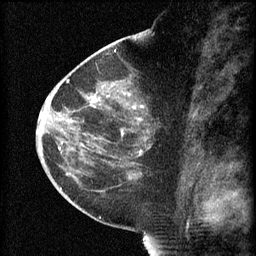
Breast MRI (dynamic contrast-enhanced), one sagittal slice. Slice 33 of 60 in the series (ordered by position). 3 images stored at this slice position (order not interpretable as contrast timing). 1.5 T. TE 4.2 ms, TR 8.2 ms. 2 mm slice thickness. 256 × 256 image matrix, field of view 180 × 180 mm. Patient: female, 44 years.
Annotated regions visible in this slice (semi-automatically segmented with operator editing):
- analysis volume of interest (the breast-tissue region the enhancement analysis was run in; not a lesion): bounding box [x1, y1, x2, y2] px = [73, 82, 168, 165]
- tumour enhancement mask (voxels above the 70 % enhancement threshold inside the analysis volume of interest): [82, 94, 144, 157]